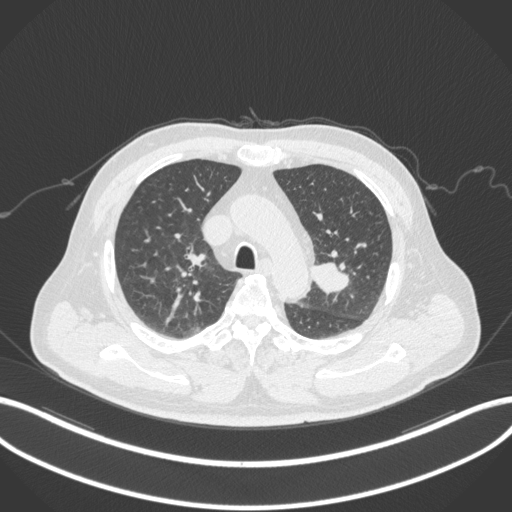
Chest CT, one axial slice; slice 216 of 286 in the series (ordered by position); reconstruction kernel B31f; lung window (W 1500 / L -600 HU); 512 × 512 image matrix, field of view 400 × 400 mm. Patient: male, 67 years. From the clinical record (not read from this slice): clinical TNM (as recorded): T2a N1 M0; histopathological grade: G3.
Outlined on this slice (bounding box drawn by a radiologist):
- lung tumour (recorded histology: adenocarcinoma): box from (x=307, y=257) to (x=355, y=297) px